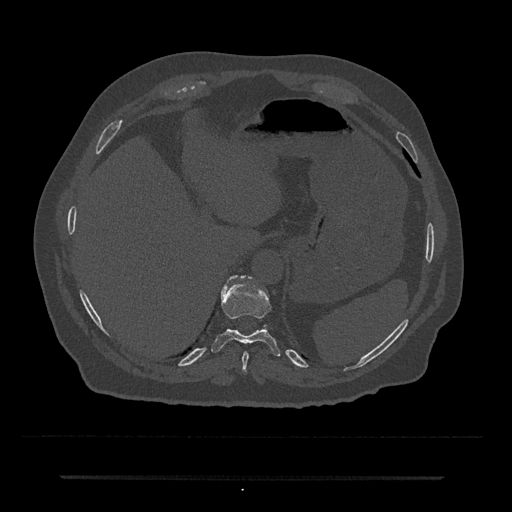
CT including the spine, one axial slice; reconstruction kernel Br40s/3; bone window (W 1800 / L 400 HU); 0.5 mm slice thickness; 512 × 512 image matrix, field of view 437 × 437 mm. Patient: male, 69 years. Case-level facts recorded for this patient, not image findings: primary cancer: prostate.
Annotated regions visible in this slice (semi-automatically segmented with operator editing):
- T10 vertebra: bounding box <211,275,281,357> (left, top, right, bottom; pixels)
- T11 vertebra: <229,275,244,281>
- T9 vertebra: <242,351,249,372>